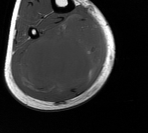
MRI of an extremity soft-tissue mass, one axial slice. Position 62 of 76 along the scan axis. MR volume resampled by the dataset authors to the PET/CT grid (not the native acquisition matrix). 3.27 mm slice thickness. 148 × 133 image matrix, field of view 145 × 130 mm. Male patient. From the clinical record (not read from this slice): histological type: liposarcoma - round cell; grade: high; site of the primary tumour: right calf.
Outlined on this slice (expert contour drawn on MRI and transferred to this co-registered scan by the dataset authors):
- gross tumour volume (mass): bounding box <13,17,103,97> (left, top, right, bottom; pixels)